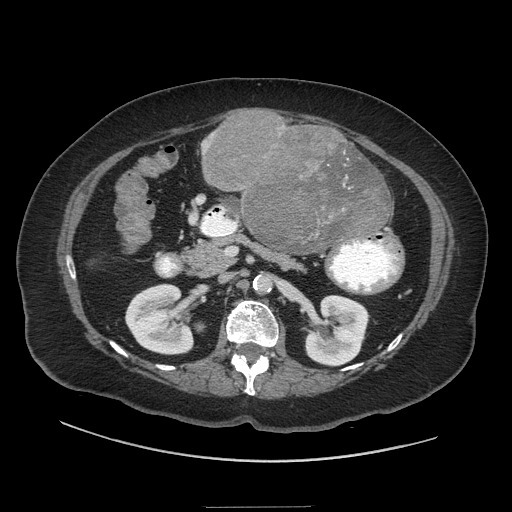
Contrast-enhanced abdominal CT (liver protocol), one axial slice; slice 5 of 81 in the series (ordered by position); 140 kVp; soft-tissue window (W 400 / L 40 HU); 2.5 mm slice thickness; 512 × 512 image matrix, field of view 440 × 440 mm. Case-level facts recorded for this patient, not image findings: diagnosis: hepatocellular carcinoma (patient treated with transarterial chemoembolisation; whether this scan precedes or follows treatment is not stated here); TNM stage (as recorded): Stage-II.
Structures marked on this image (semi-automatically segmented with operator editing):
- liver parenchyma outside the tumour (the mass and vessels are separate outlines, so this box may not span the whole liver): bounding box (x1, y1, x2, y2) in pixels: (91, 122, 394, 264)
- mass: (202, 112, 388, 251)